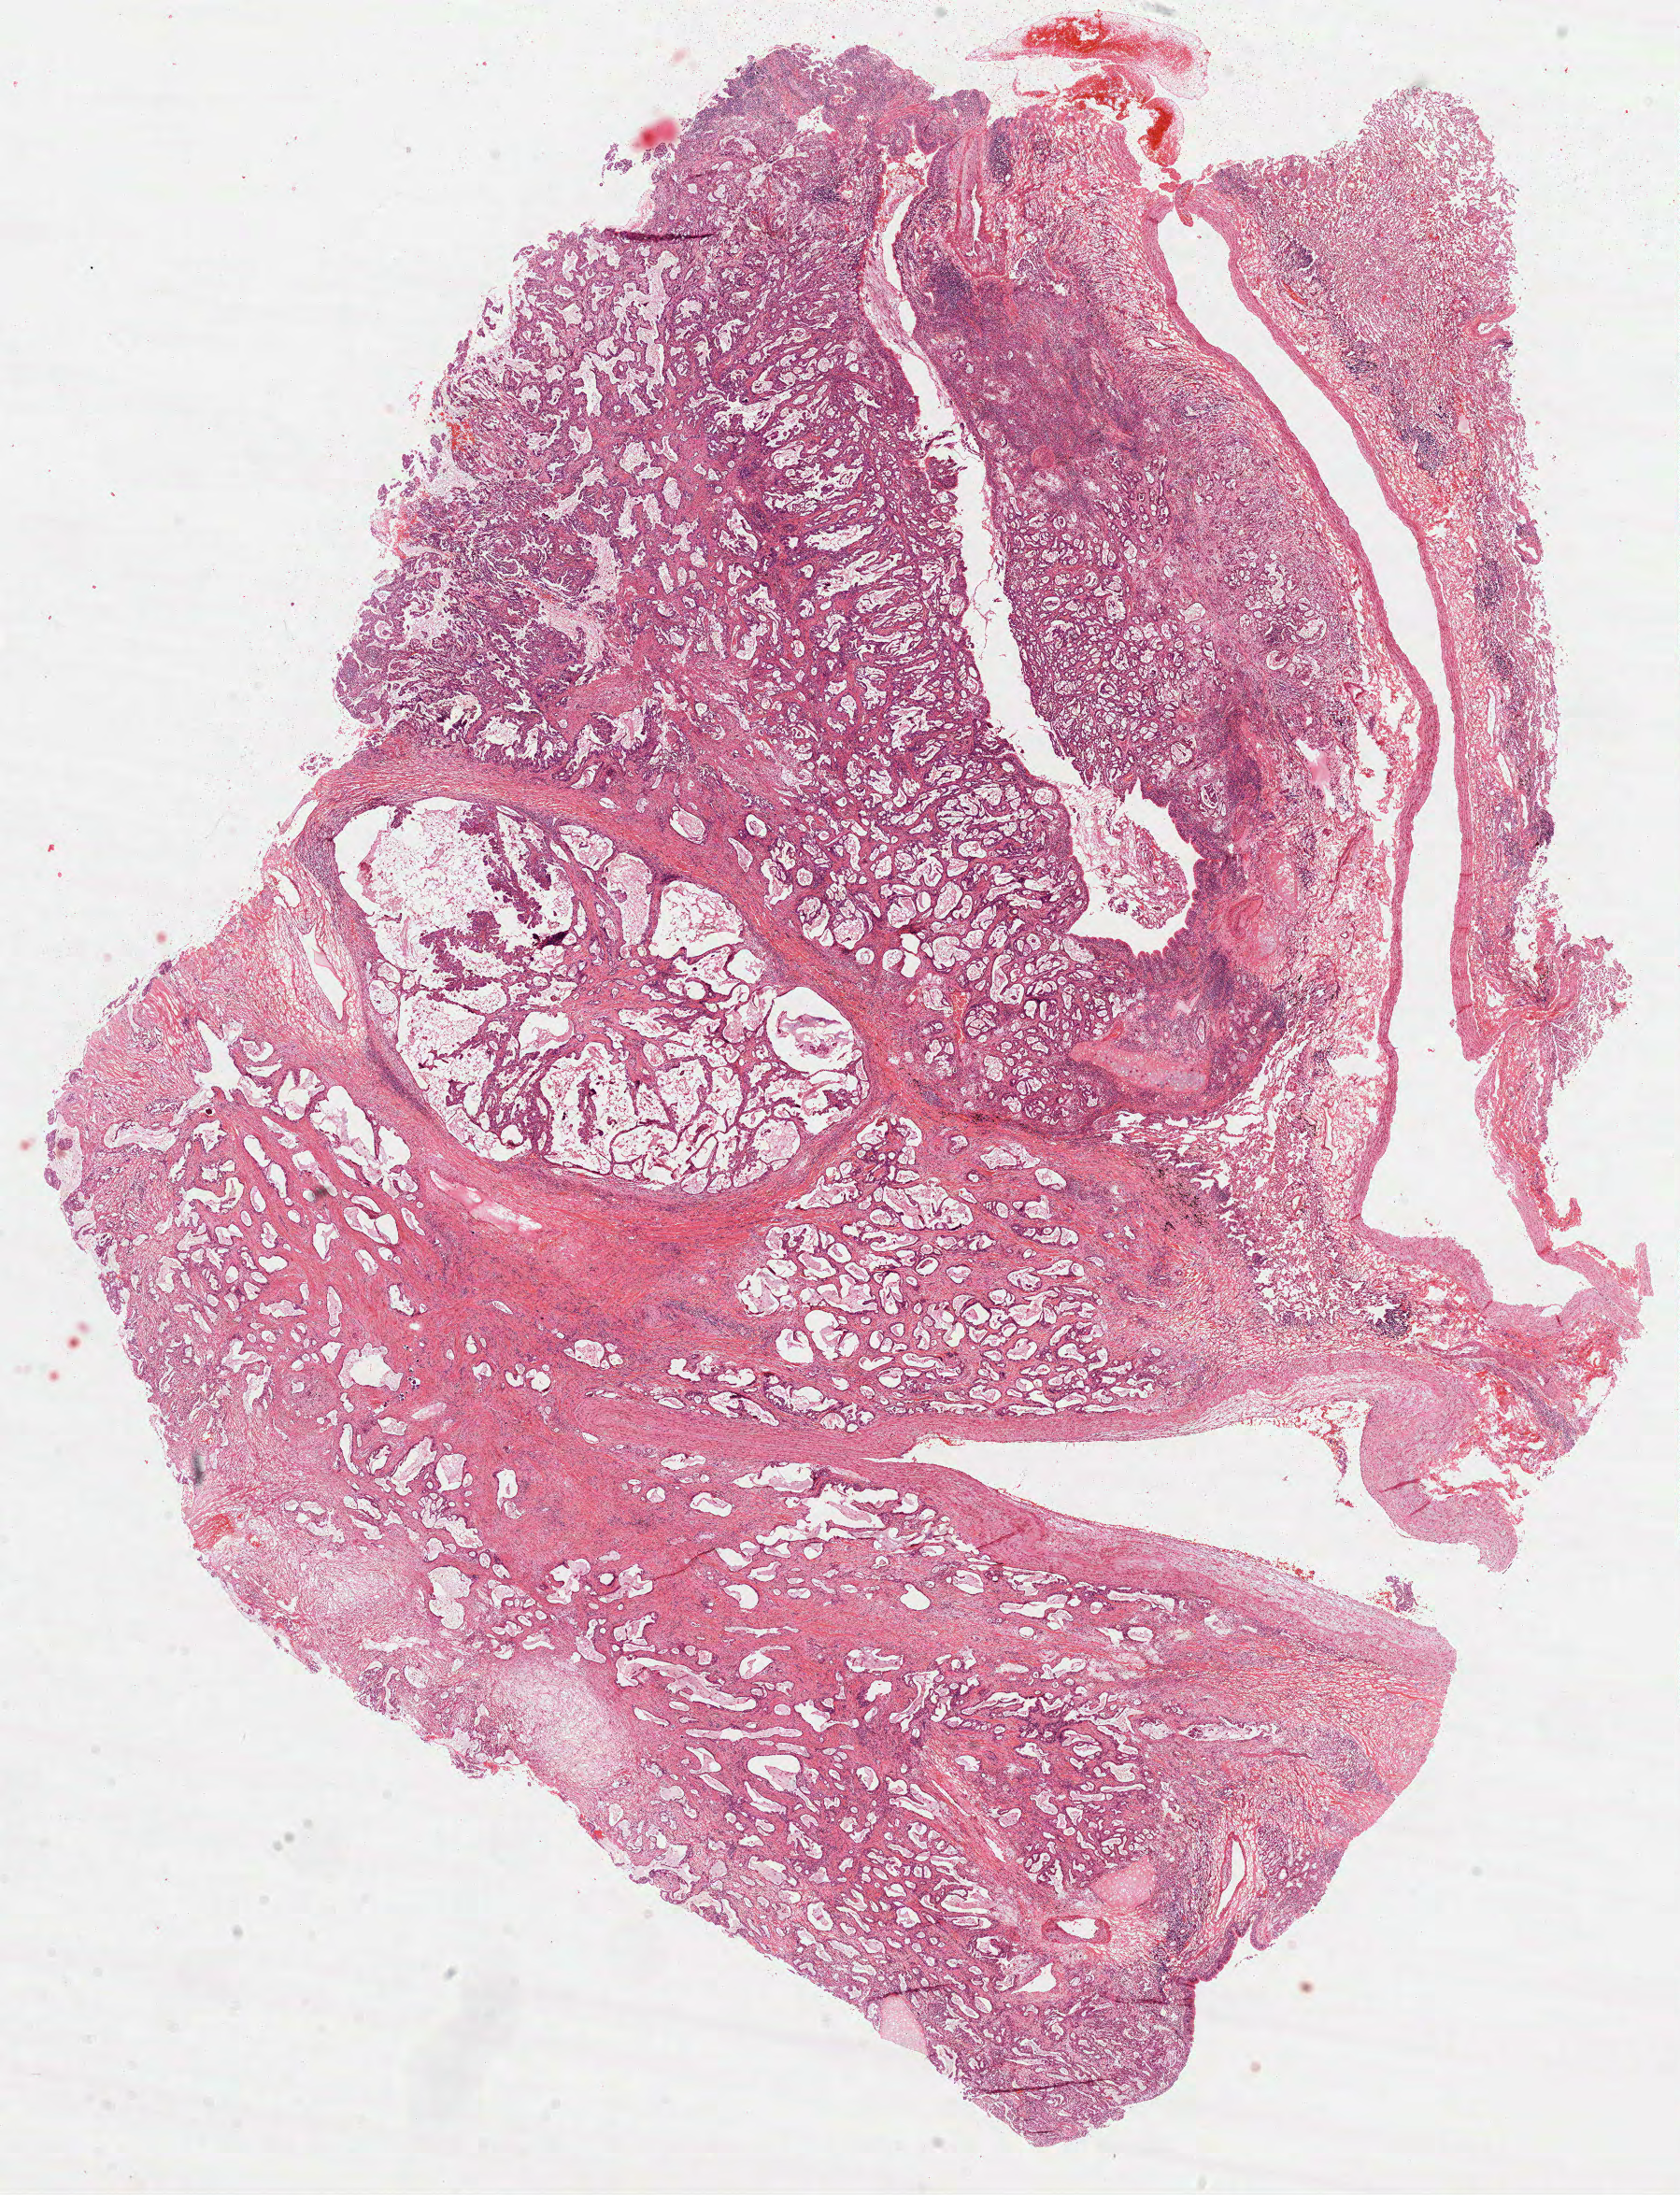
Digitized H&E tissue section (whole slide) — low-resolution overview of the scanned area, about 14.5 x 18.9 mm (from a 40x scan). Formalin-fixed paraffin-embedded (FFPE) diagnostic section. Sample: primary tumour, lung. Male patient; age at initial diagnosis 50 years.
AJCC pathologic stage: IIA (7th edition). Histologic diagnosis: Papillary adenocarcinoma, NOS. Laterality: right.